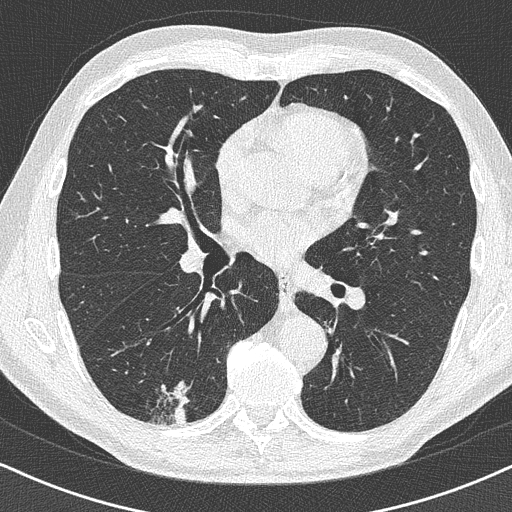
Low-dose screening chest CT, one axial slice. Slice 226 of 438 in the series (ordered by position). 120 kVp. Lung window (W 1500 / L -600 HU). 1 mm slice thickness. 512 × 512 image matrix, field of view 320 × 320 mm.
Annotated regions visible in this slice (outlined manually by an expert reader):
- lesion 1 (tumor, lower lobe of right lung): box from (x=174, y=407) to (x=187, y=425) px